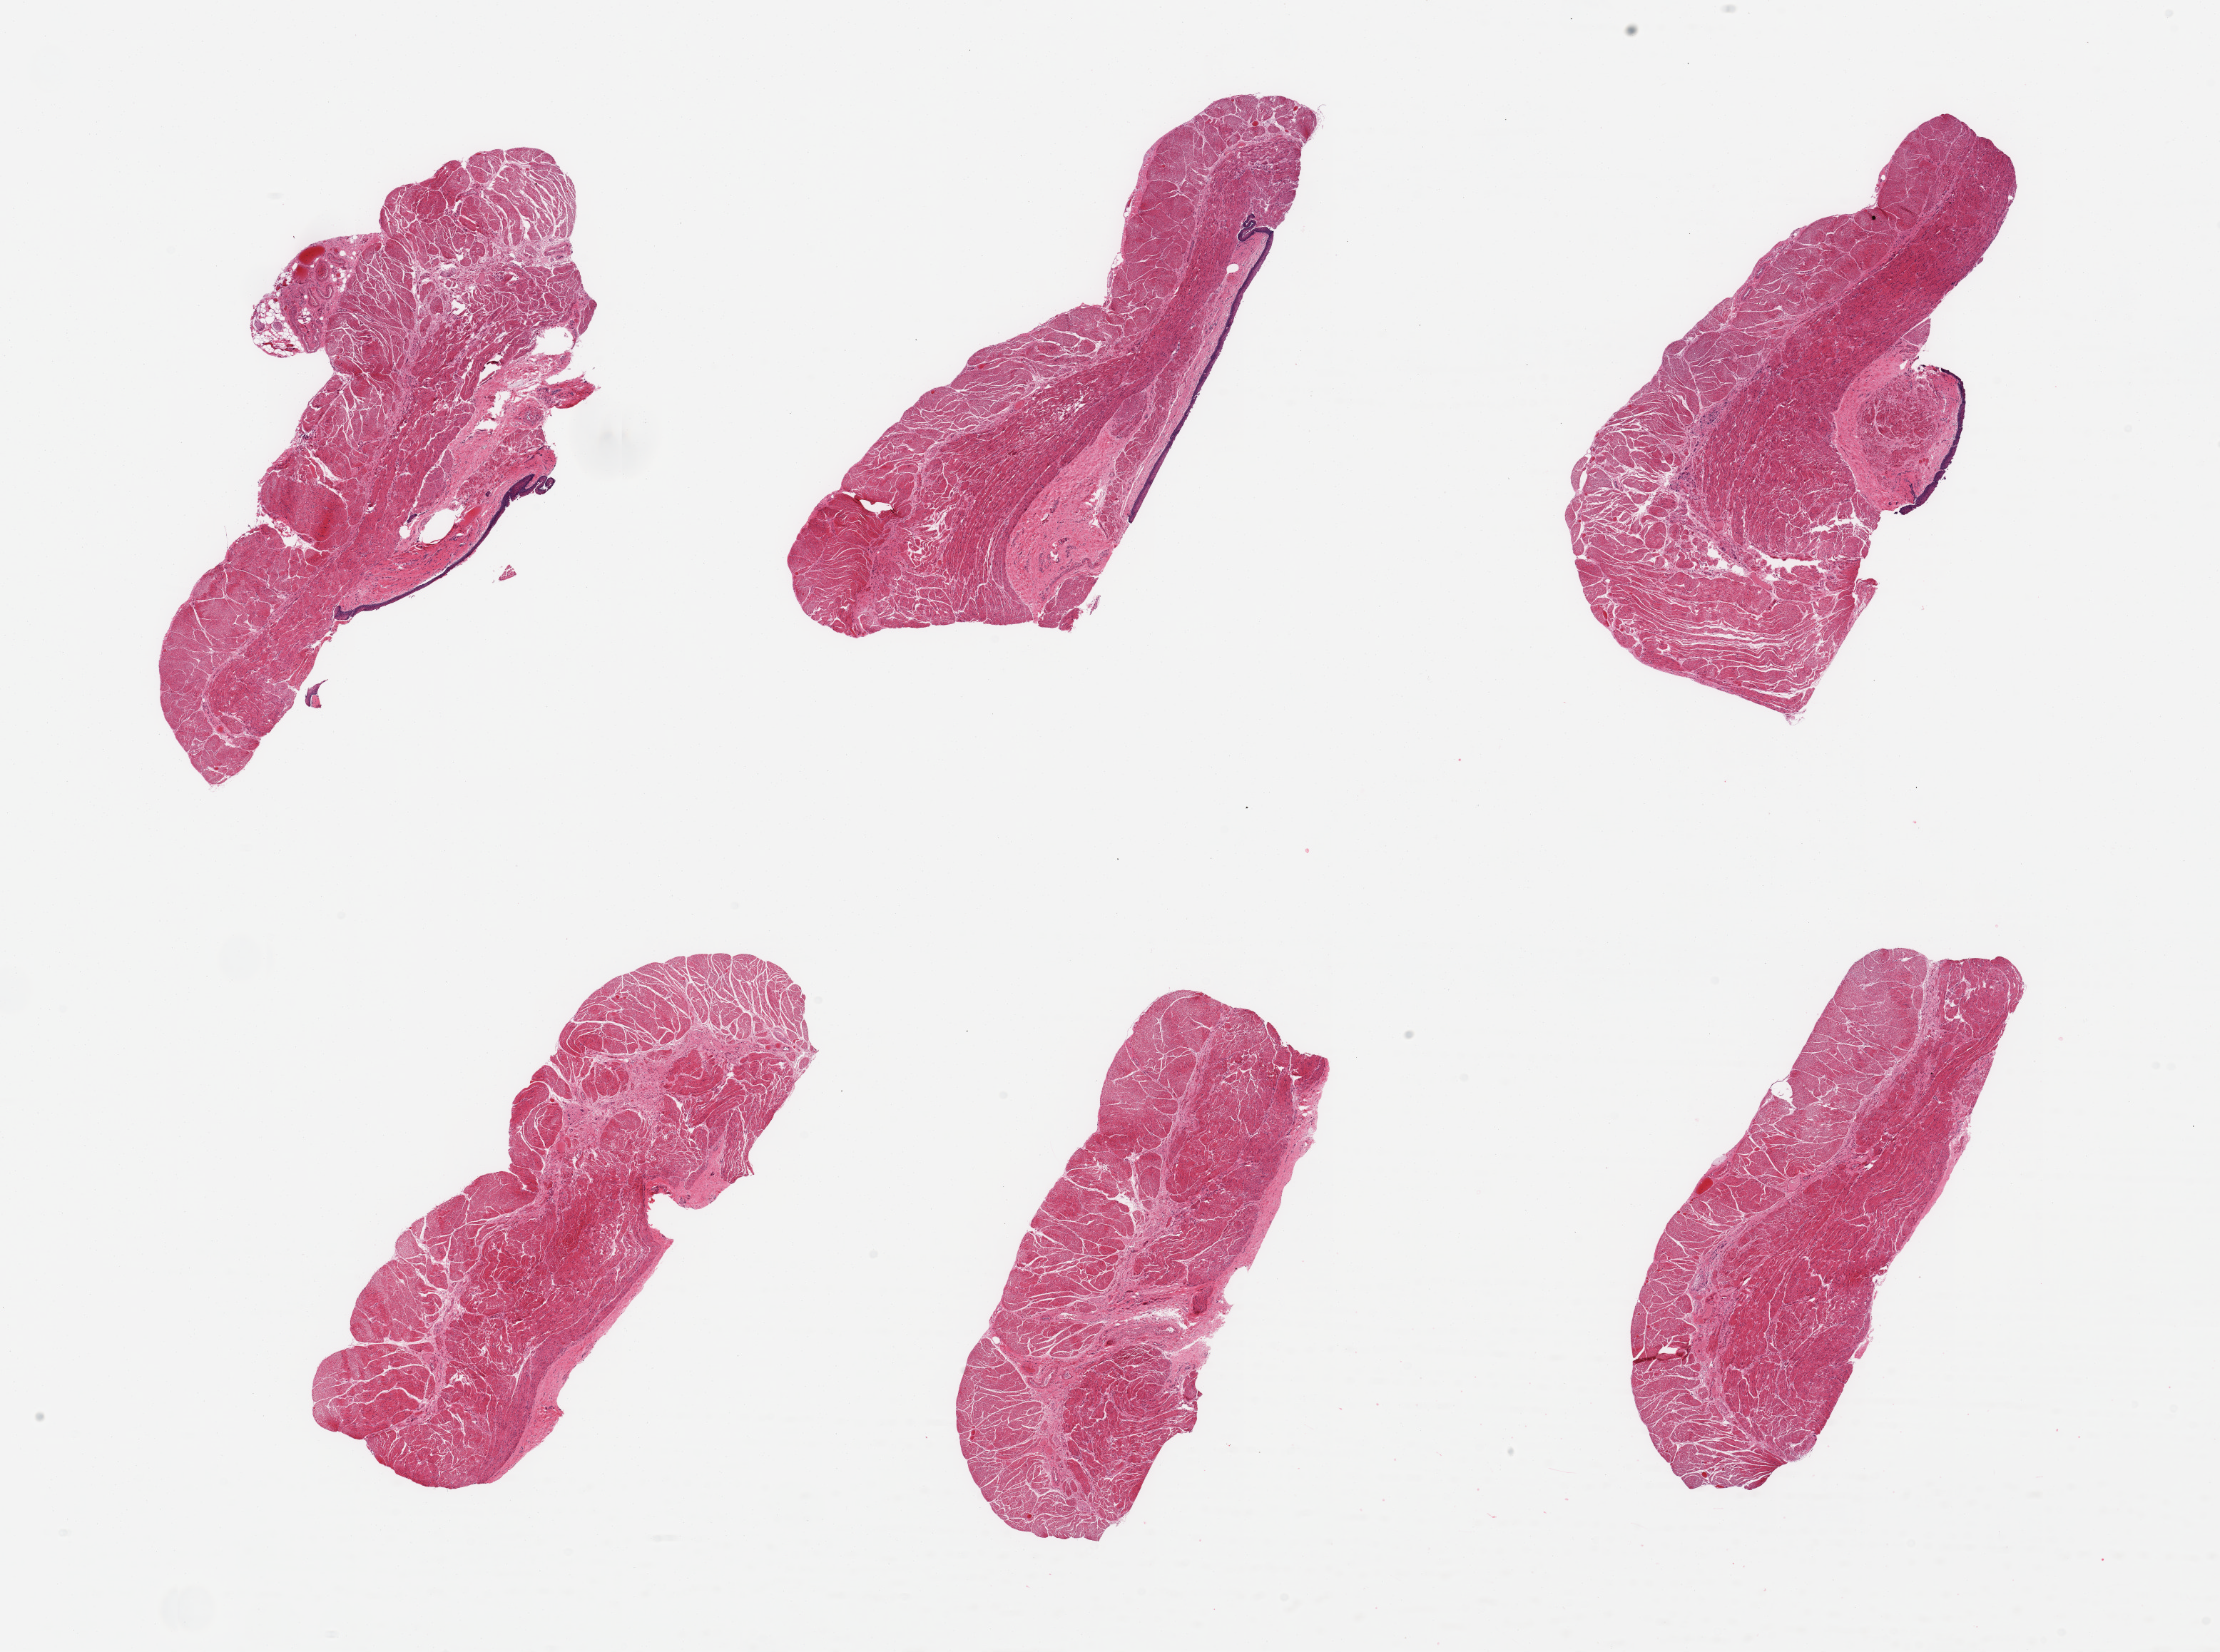
H&E whole-slide image, whole scanned area (about 24.6 x 18.3 mm) shown as a low-resolution overview. PAXgene-fixed, paraffin-embedded tissue. Sampled site (target tissue): gastroesophageal junction. Tissue donor sample. Female donor.
• reviewer comment on this tissue sample: 6 pieces; mostly target muscularis, 3 of 6 pieces include residual squamous epithelium